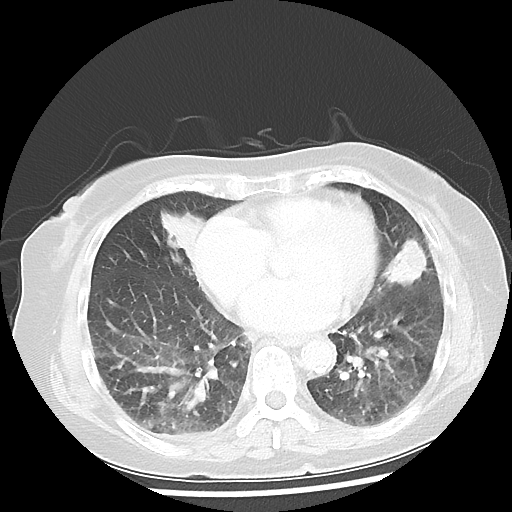
Chest CT, one axial slice. Position 18 of 50 along the scan axis. Reconstruction kernel LUNG. Lung window (W 1500 / L -600 HU). 5 mm slice thickness. 512 × 512 image matrix, field of view 332 × 332 mm. Patient: female, 77 years. From the clinical record (not read from this slice): clinical TNM (as recorded): T2 N3 M1a.
Annotated regions visible in this slice (rectangle marked by the reading radiologist):
- lung tumour (recorded histology: adenocarcinoma): bounding box <386,236,430,289> (left, top, right, bottom; pixels)